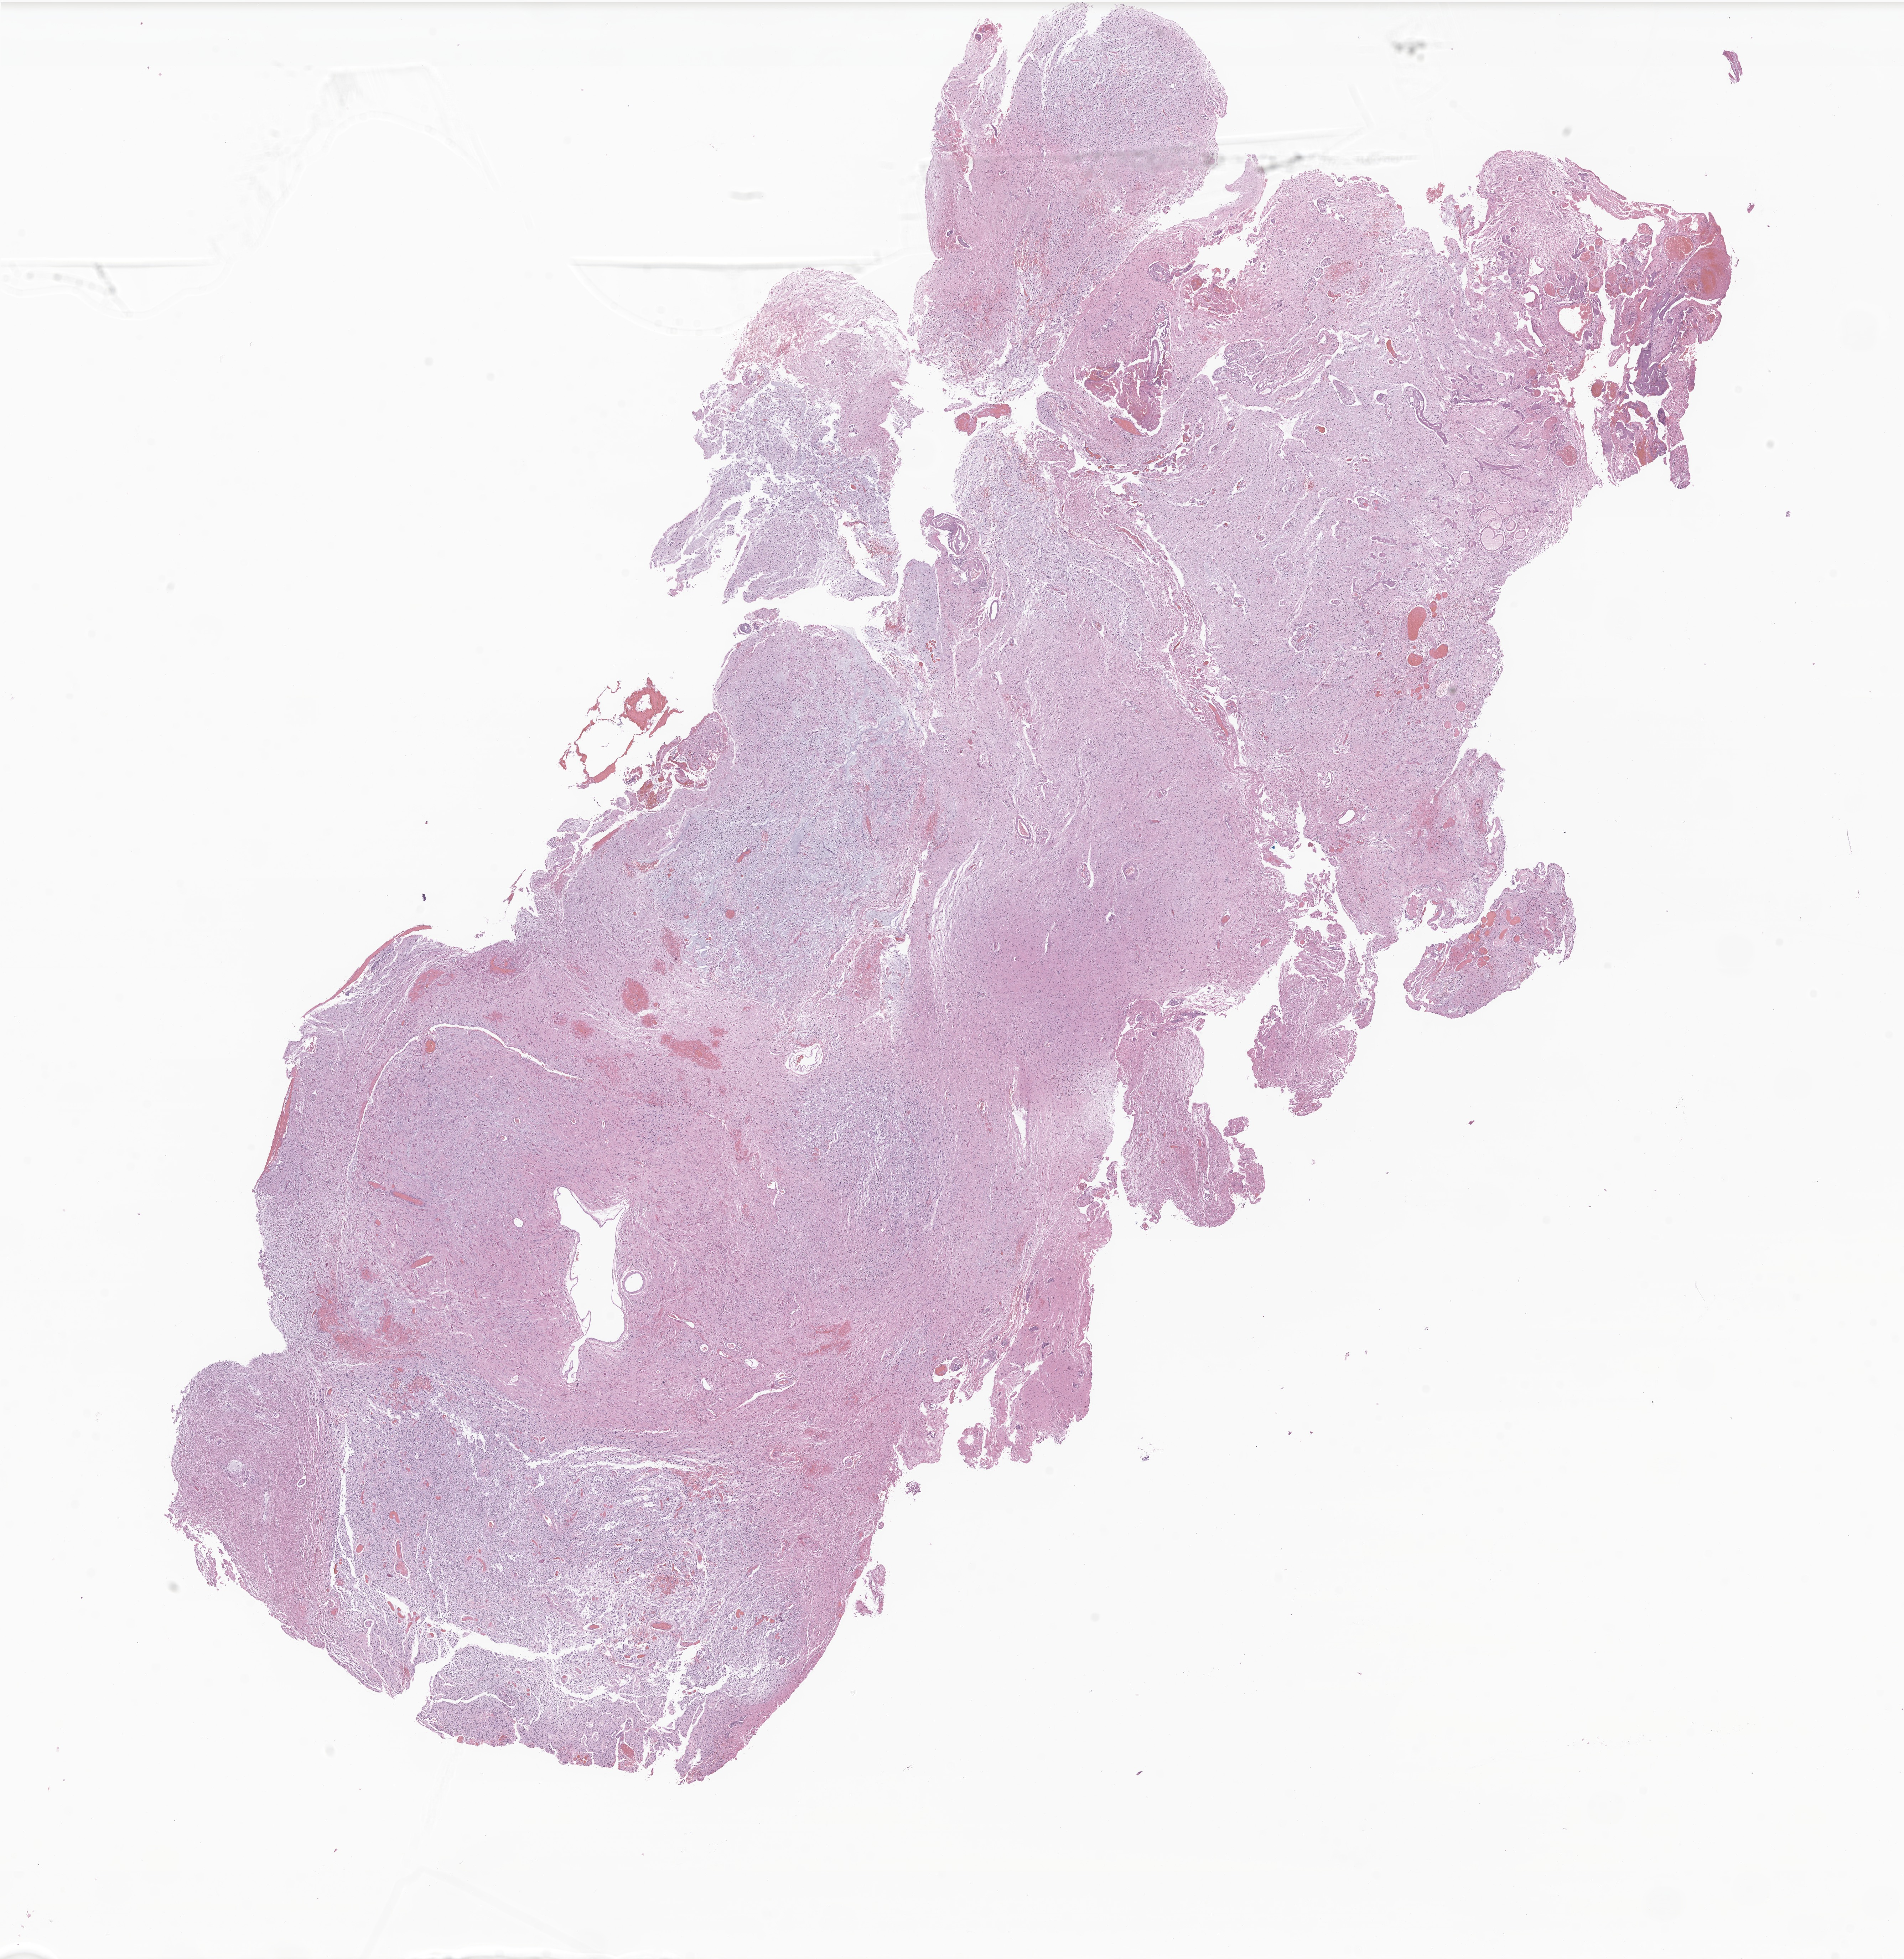
Digitized haematoxylin and eosin-stained section of tumor tissue from the brain — whole scanned area (about 22.5 x 23.2 mm) shown as a low-resolution overview, formalin-fixed paraffin-embedded section. Patient: female, age 169 months (14 years 1 month).
- recorded diagnosis: Medulloblastoma, NOS